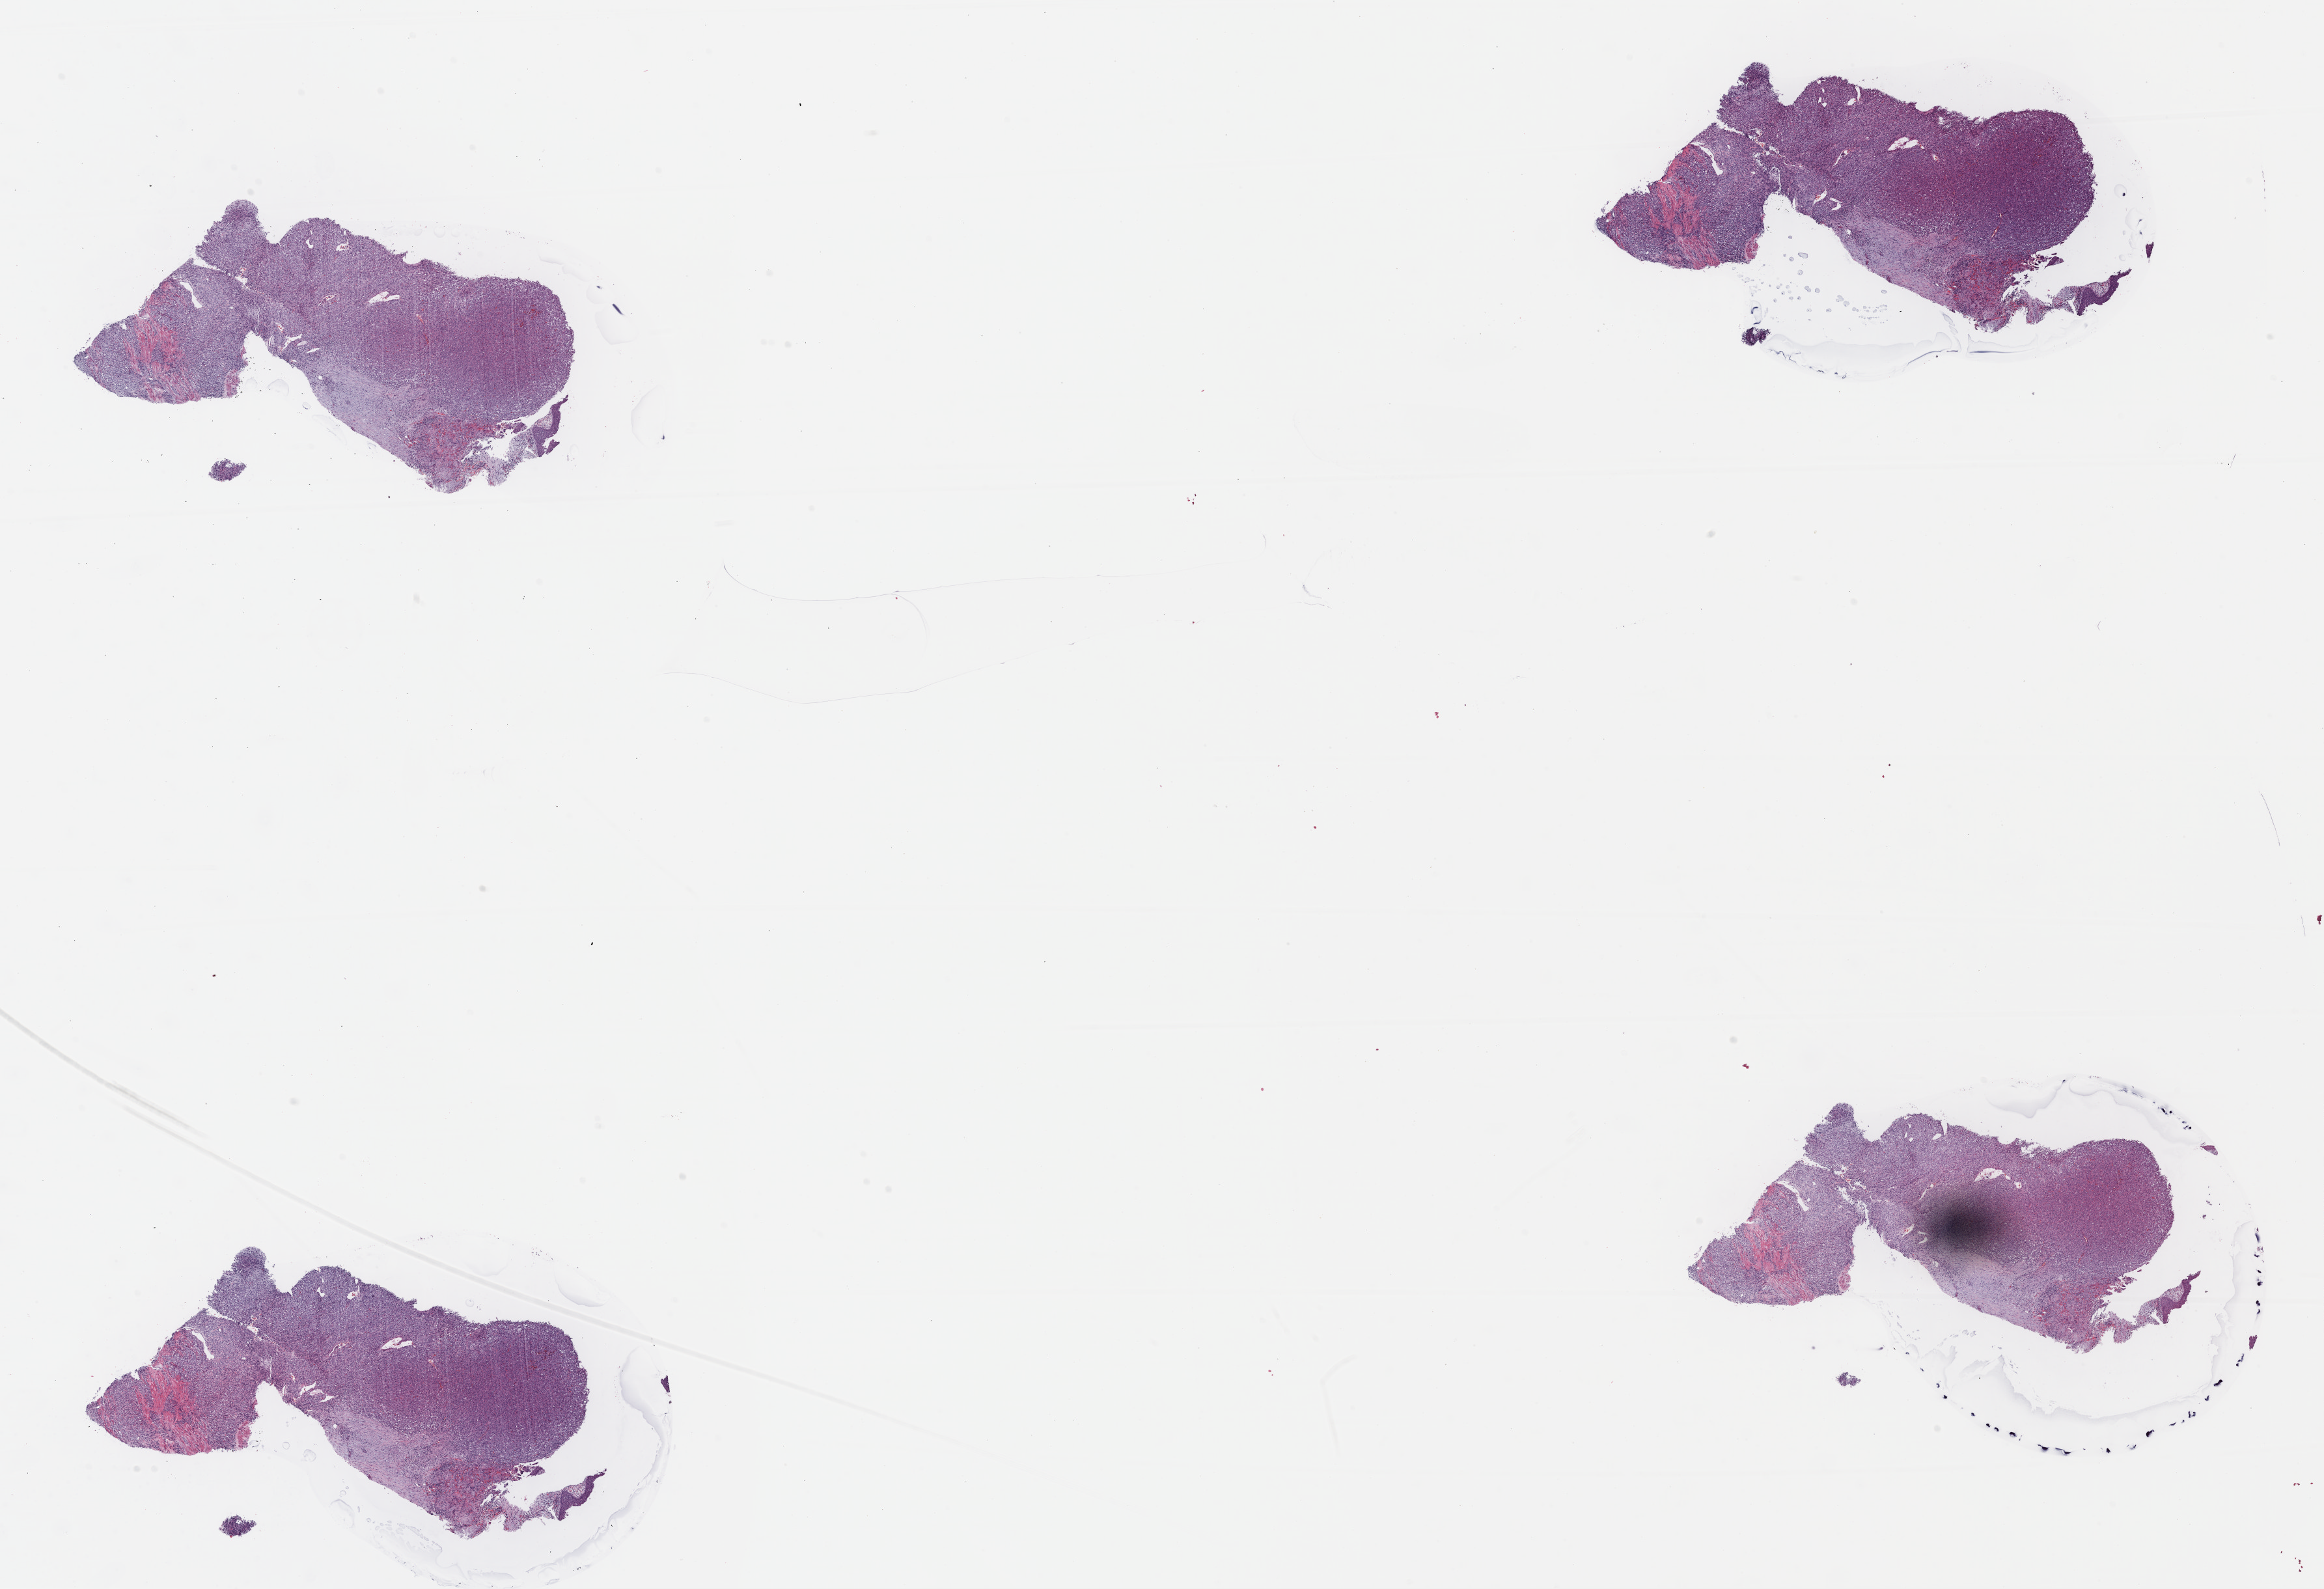
Digitized H&E tissue section (whole slide), a low-resolution overview of the entire scanned area, about 28.1 x 19.2 mm; formalin-fixed paraffin-embedded (FFPE) diagnostic section; sample: primary tumour, bladder. Female, age 57 years at initial diagnosis. Histologic grade: high grade.
AJCC pathologic stage: III (7th edition). Lymph nodes positive (case pathology): 0 of 12 examined. Pathologic diagnosis: Transitional cell carcinoma.